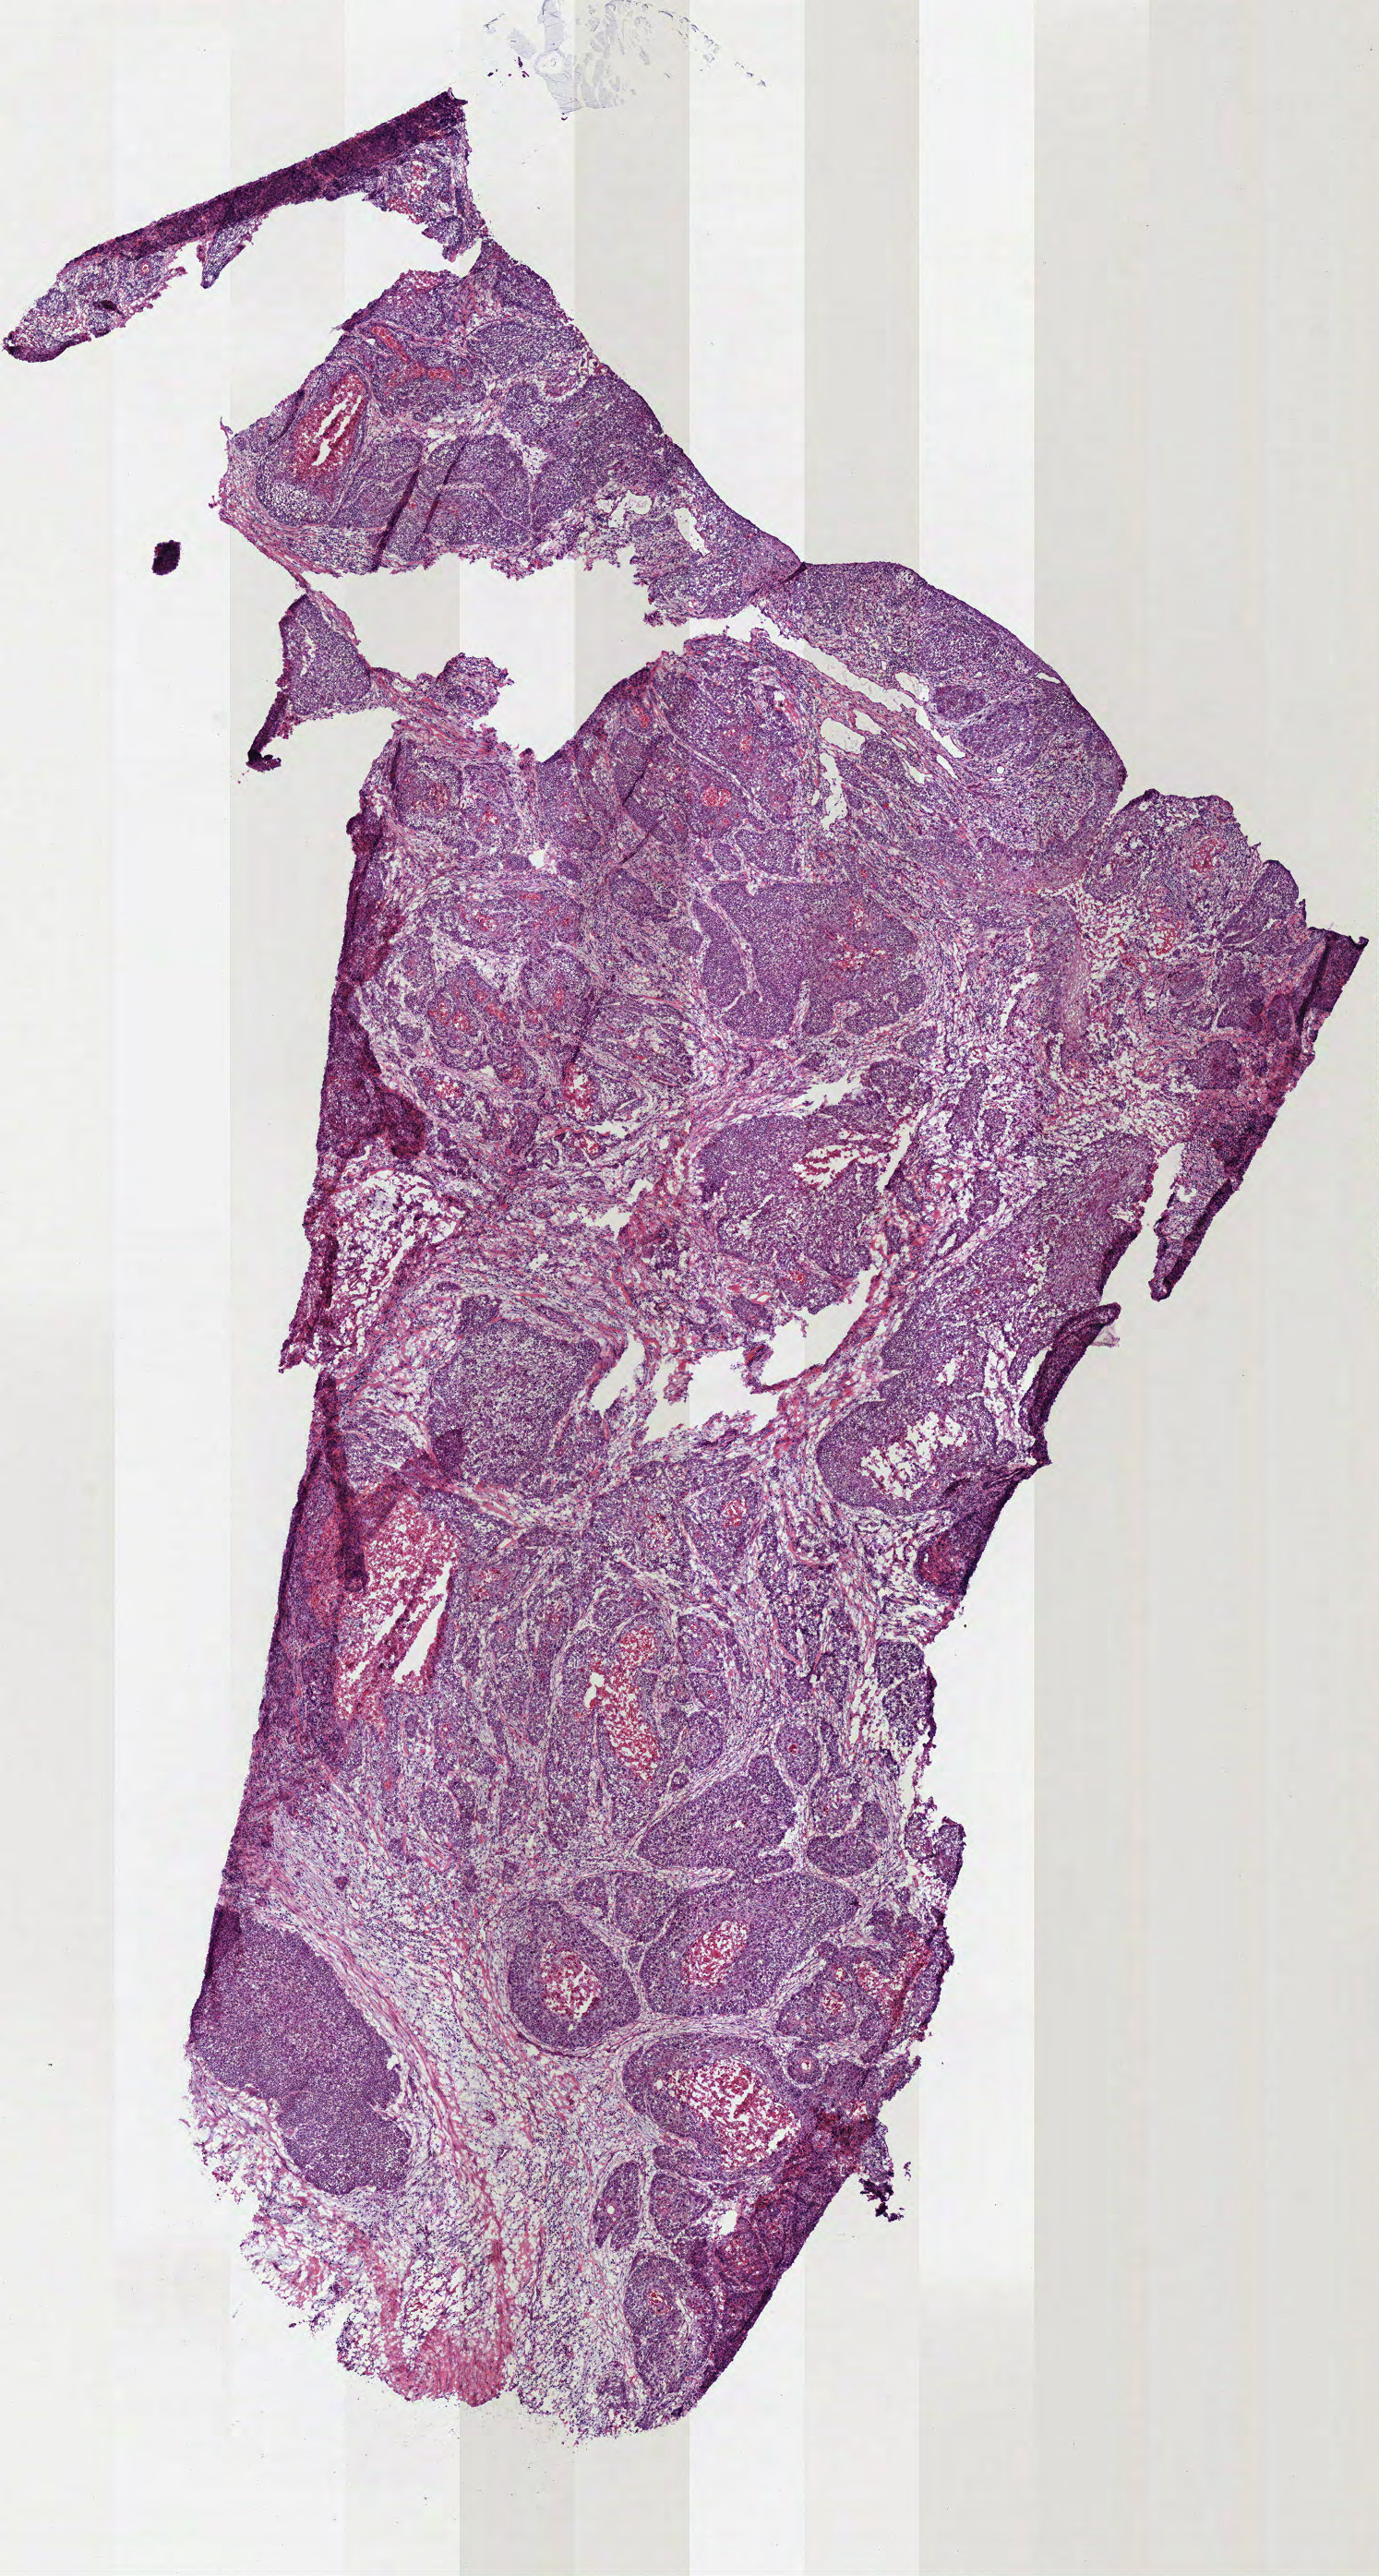
Whole-slide histology image, H&E, shown as a low-resolution overview of the whole scanned area (about 5.9 x 11.0 mm, acquisition: 40x scan); frozen section from the top of the tissue portion; sample: primary tumour, head and neck. Patient: male, age at initial diagnosis 61 years. Histologic grade: G2 (moderately differentiated). Slide review estimates, as recorded: tumour cells 82%, tumour nuclei 70%, normal cells 0%, stromal cells 18%, necrosis 0%.
- AJCC pathologic stage: IVA
- histologic diagnosis: Squamous cell carcinoma, NOS
- lymph nodes positive (case pathology): 3 of 48 examined